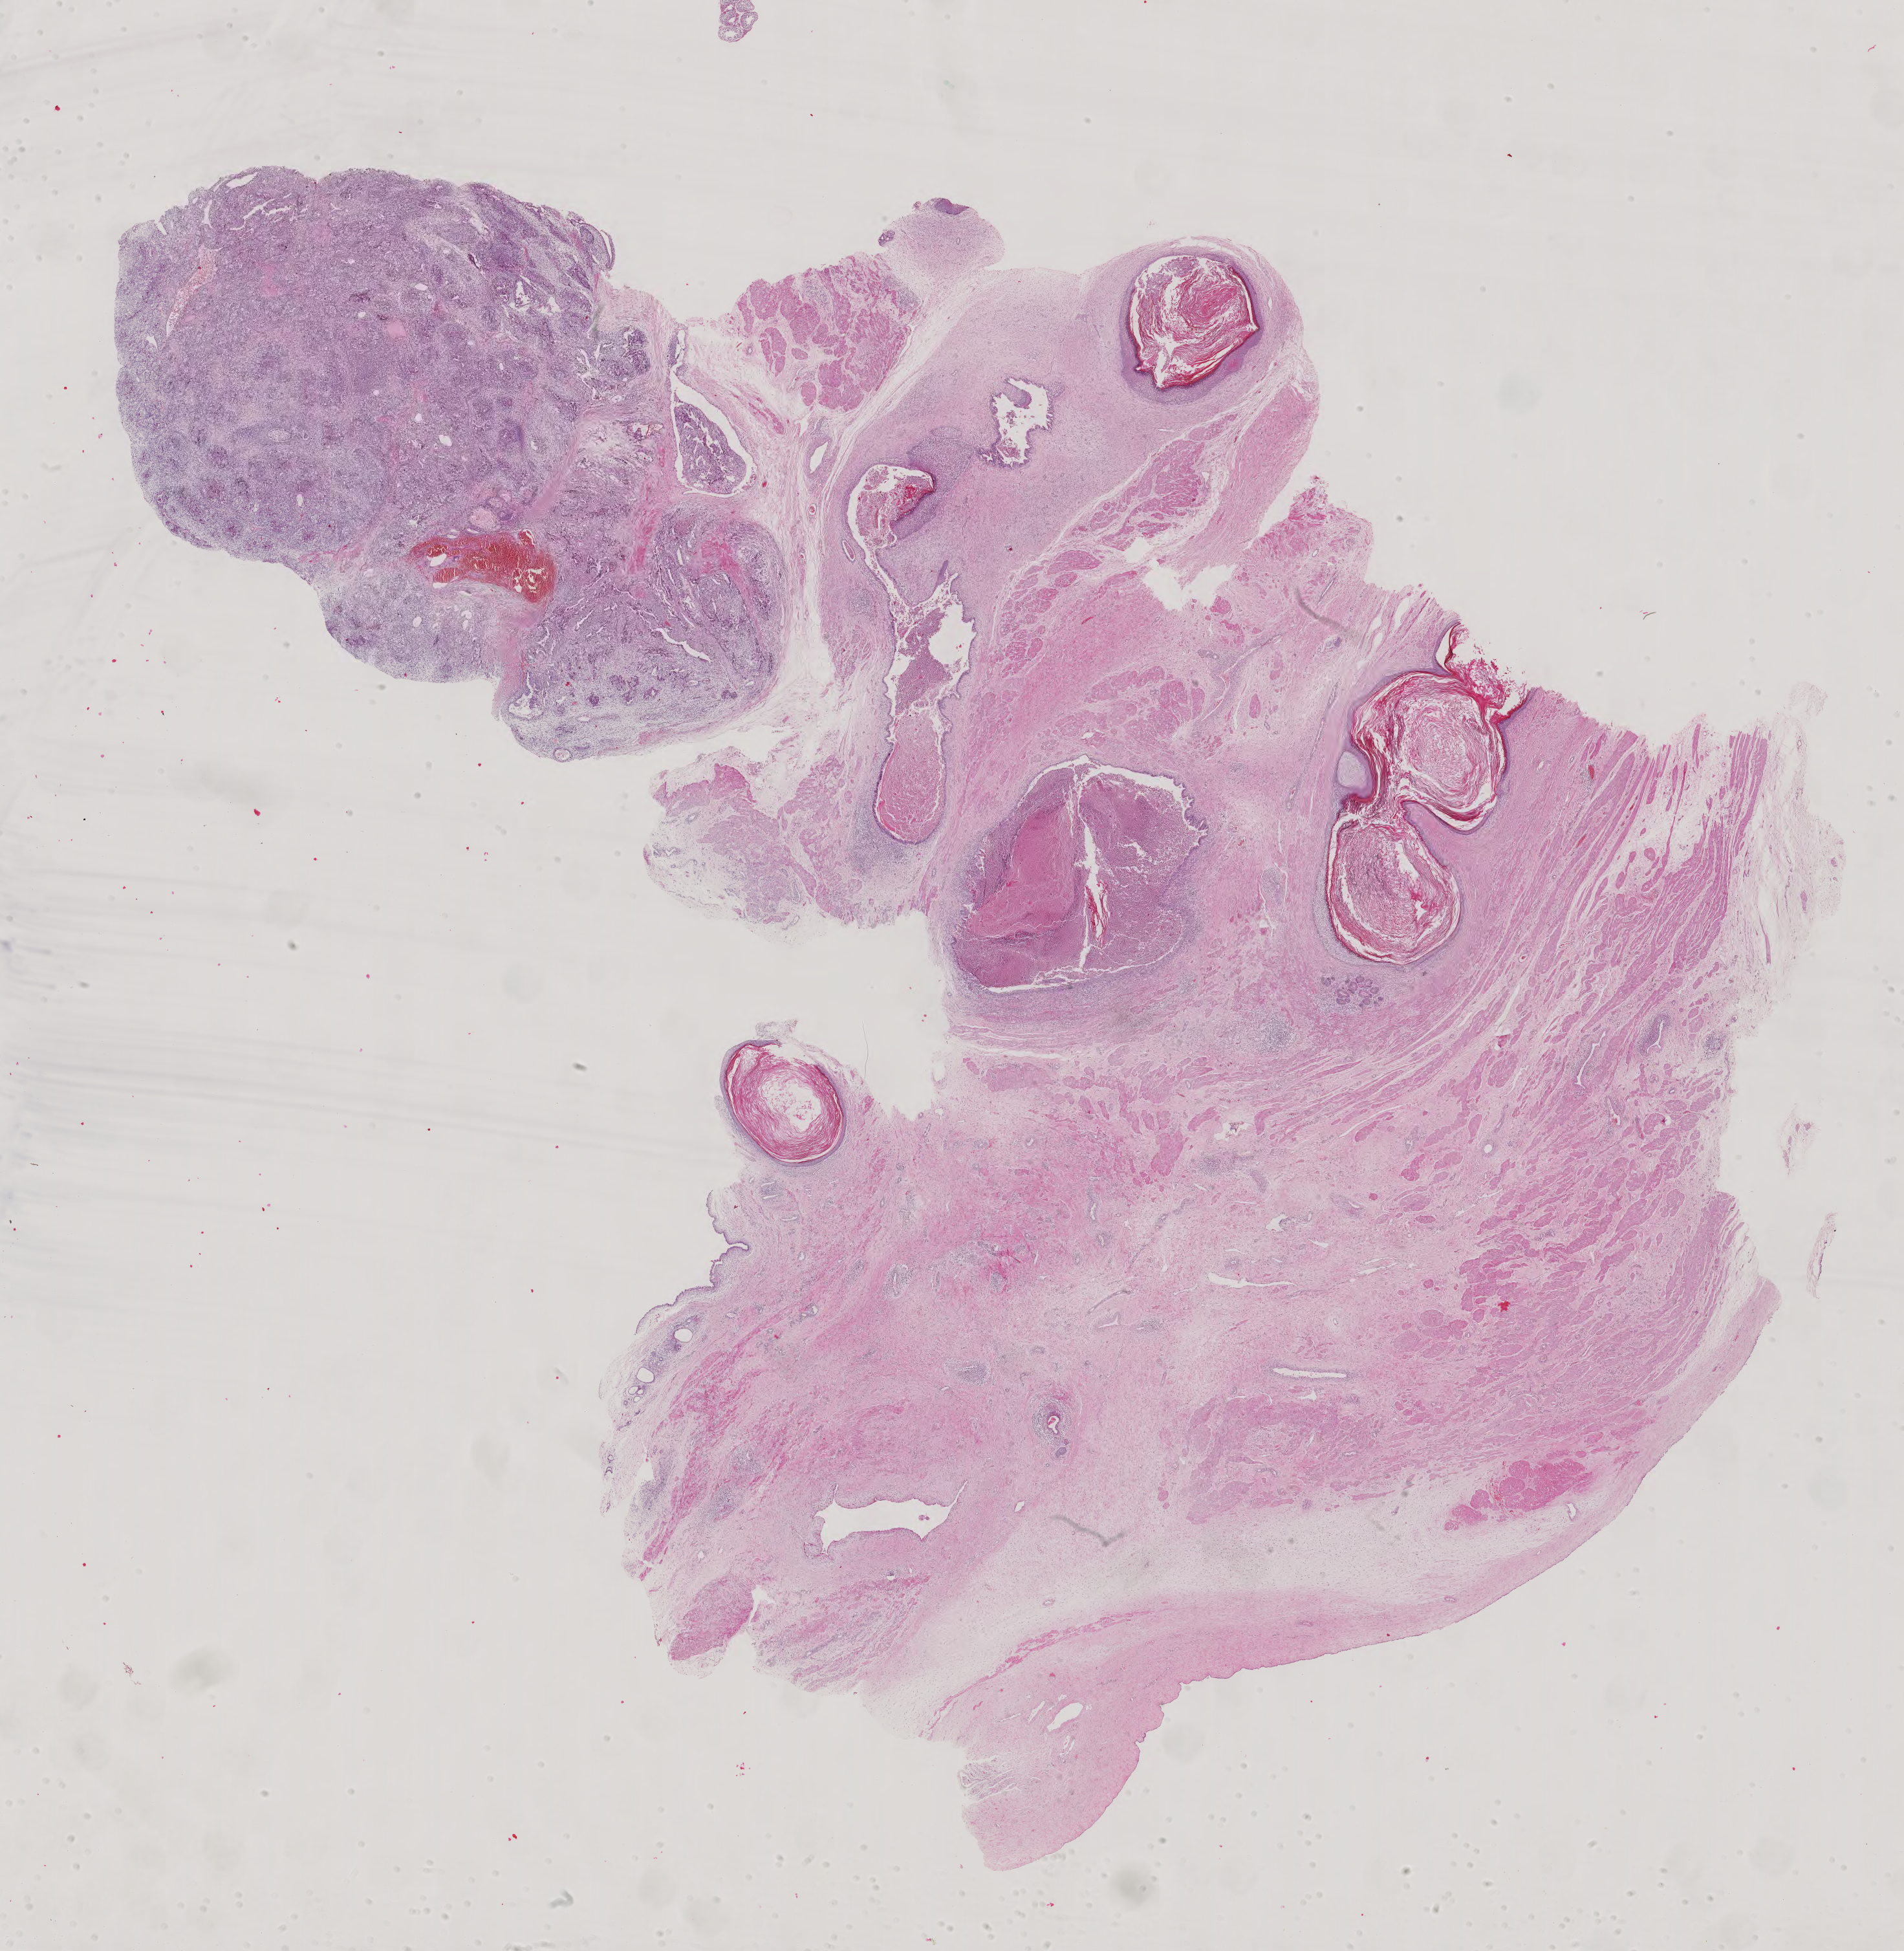
Digitized Hematoxylin and eosin (H&E) stained tissue section (whole slide), whole scanned area (about 21.5 x 22.0 mm) shown as a low-resolution overview, formalin-fixed paraffin-embedded (FFPE) diagnostic section, sample: primary tumour, testis. Male, age 24 years at initial diagnosis.
• diagnosis: Teratoma, benign
• AJCC pathologic stage: IS
• TNM: T1 N0 M0
• laterality: left